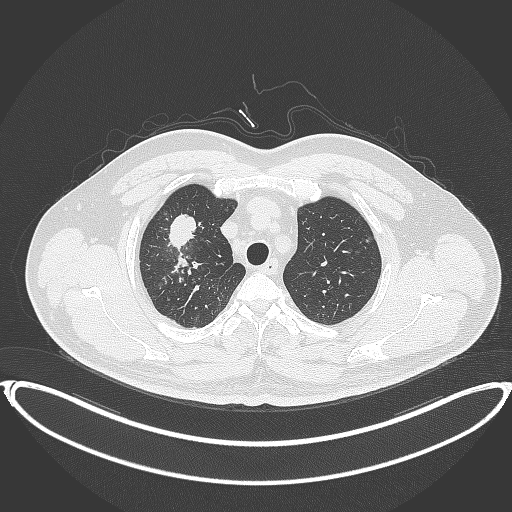
Chest CT, one axial slice. Position 315 of 399 along the scan axis. 120 kVp. Lung window (W 1500 / L -600 HU). 1 mm slice thickness. 512 × 512 image matrix, field of view 445 × 445 mm. Male patient, age 53 years. Case-level facts recorded for this patient, not image findings: clinical TNM (as recorded): T2a N0 M0.
Annotated regions visible in this slice (rectangle marked by the reading radiologist):
- lung tumour (recorded histology: adenocarcinoma): bounding box <166,207,199,253> (left, top, right, bottom; pixels)